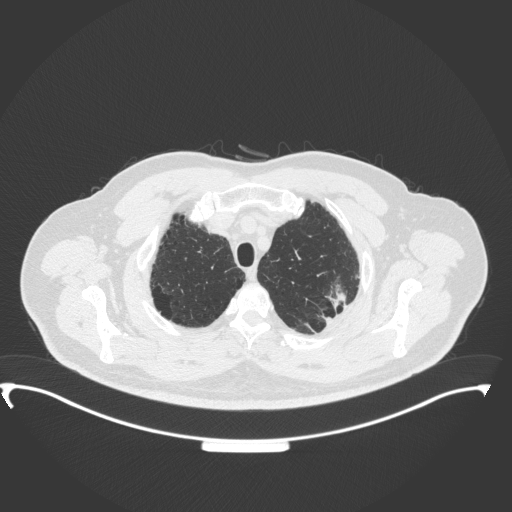
Chest CT, one axial slice; position 311 of 350 along the scan axis; reconstruction kernel B31f; 120 kVp; lung window (W 1500 / L -600 HU); 1 mm slice thickness; 512 × 512 image matrix. Patient: male, 64 years. Case-level facts recorded for this patient, not image findings: clinical TNM (as recorded): T1c N1 M1.
Structures marked on this image (bounding box drawn by a radiologist):
- lung tumour (recorded histology: adenocarcinoma): box from (x=321, y=278) to (x=348, y=314) px